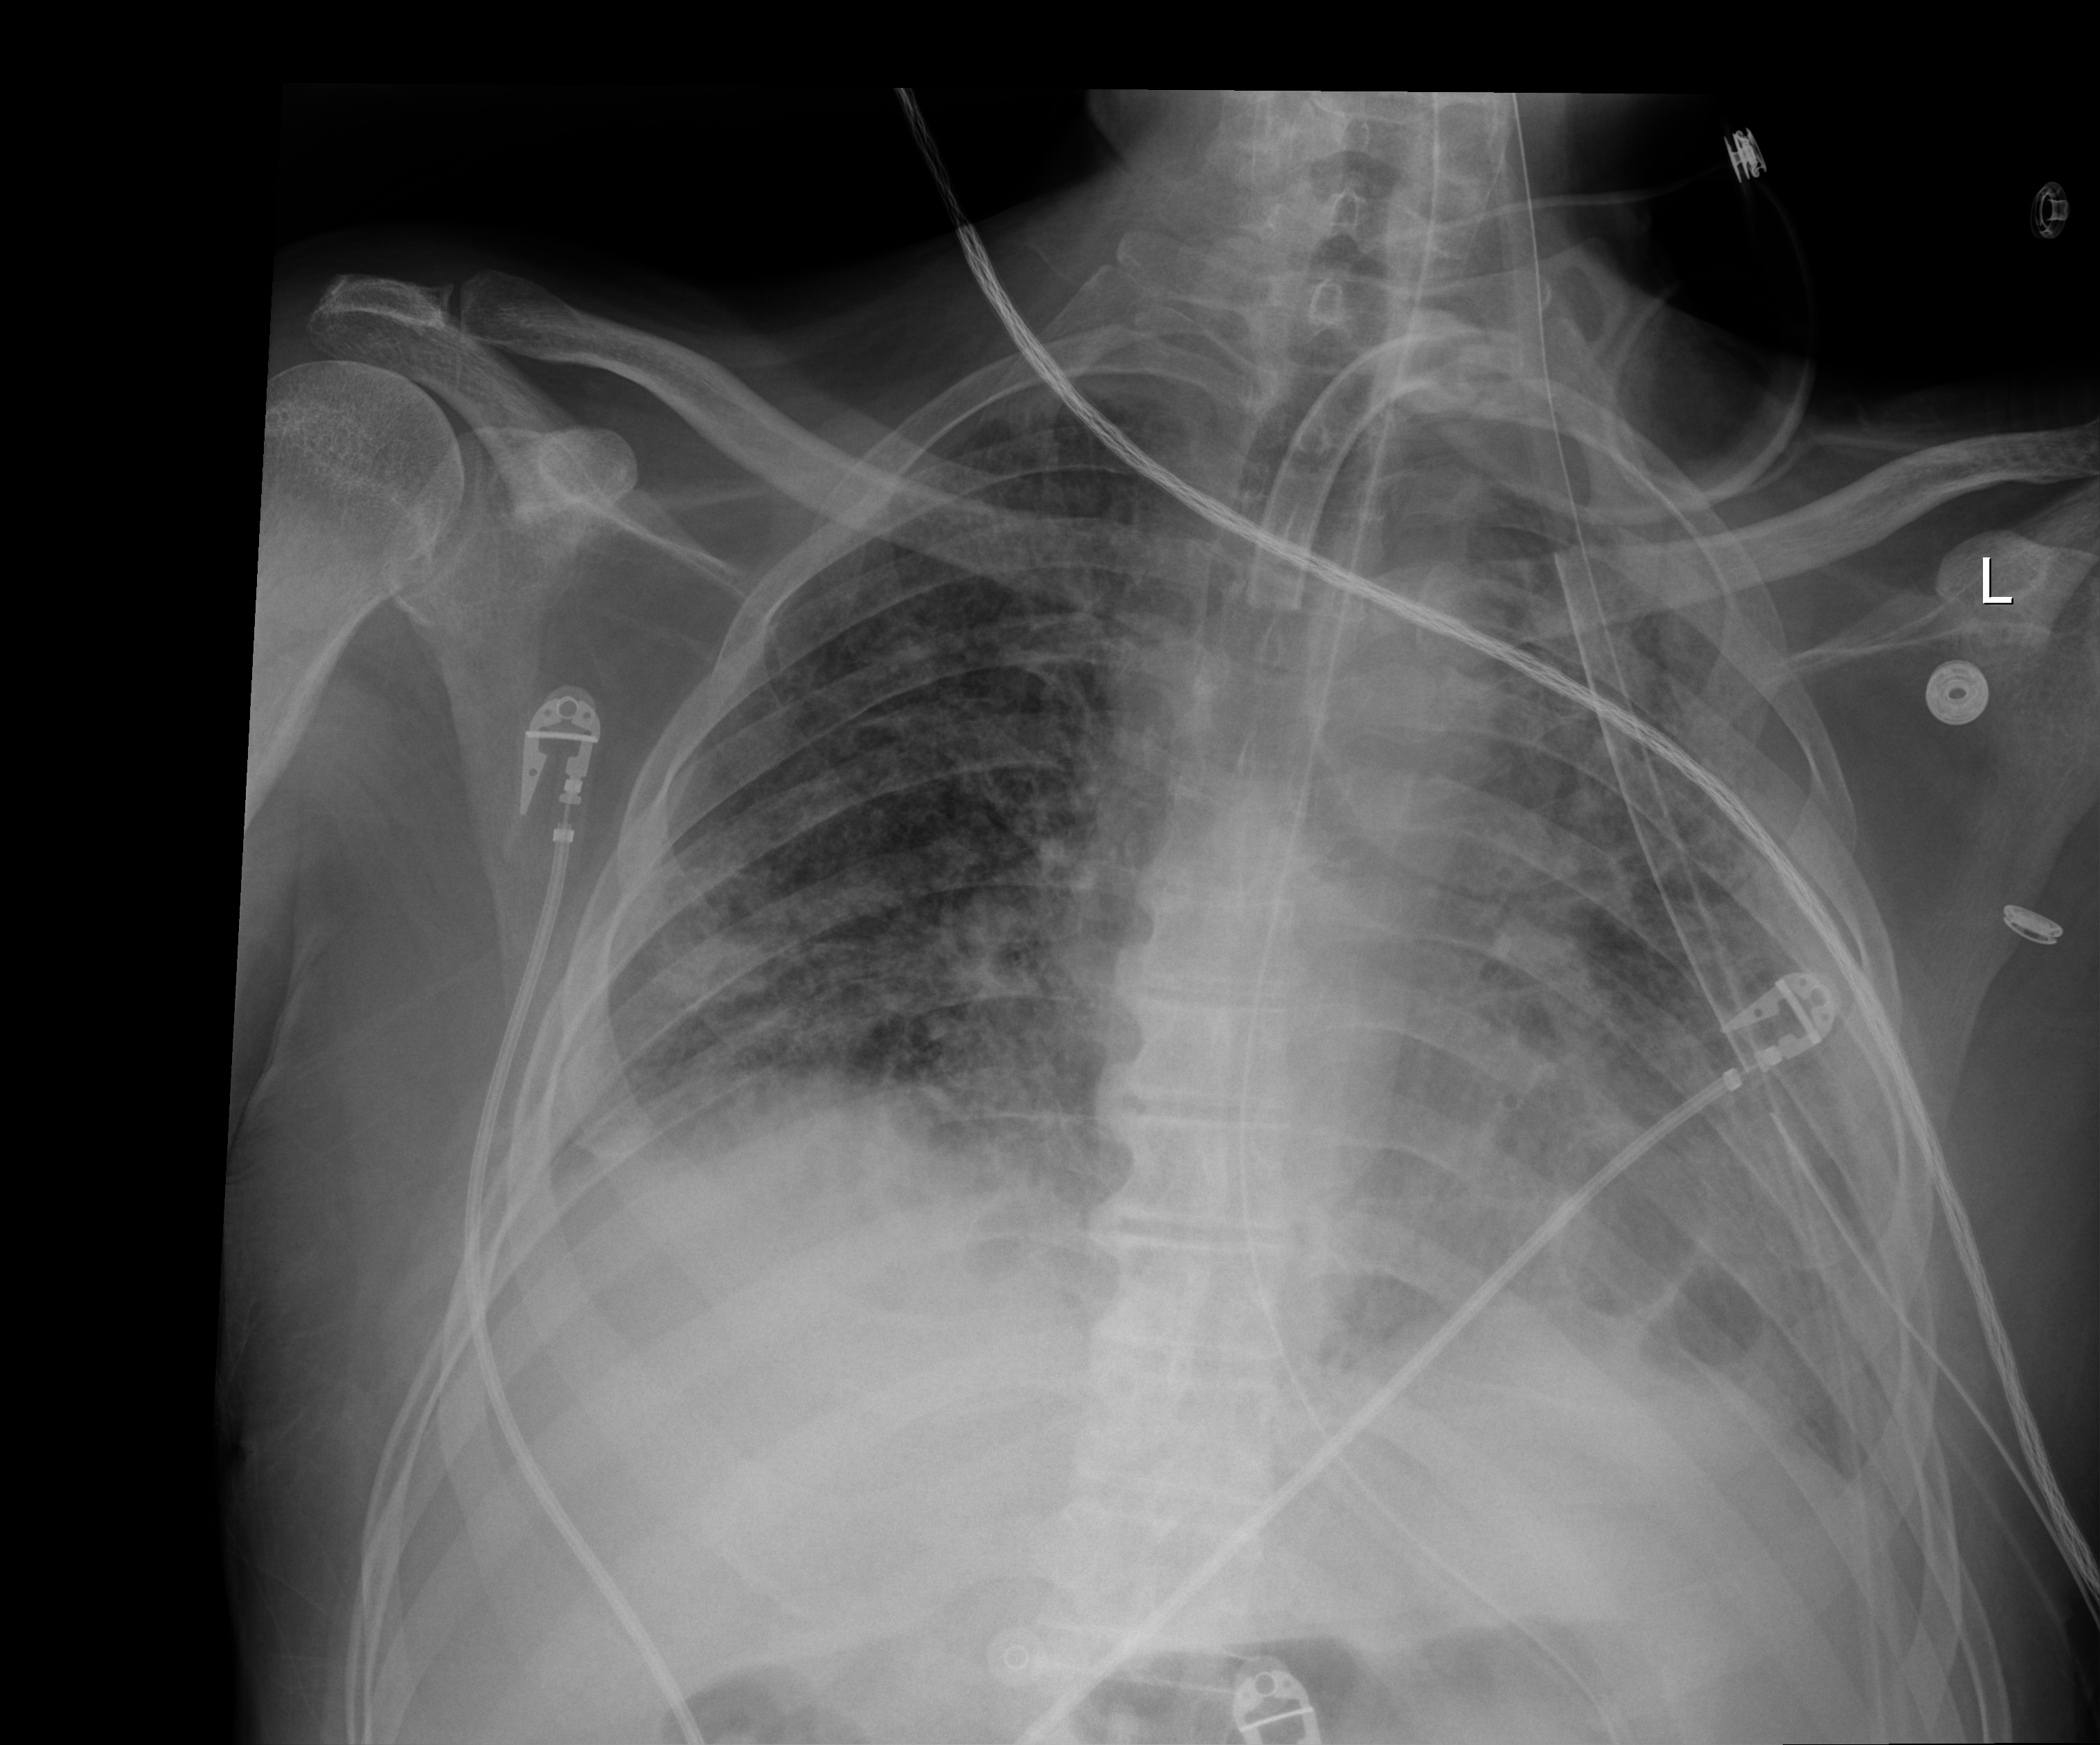
Chest X-ray (portable). Male patient hospitalised with COVID-19, age 18–59 years.
From the hospital-stay record, not from the radiograph (when in the stay this image was taken is not recorded):
- COPD (admission record): no
- length of hospital stay: 83 days